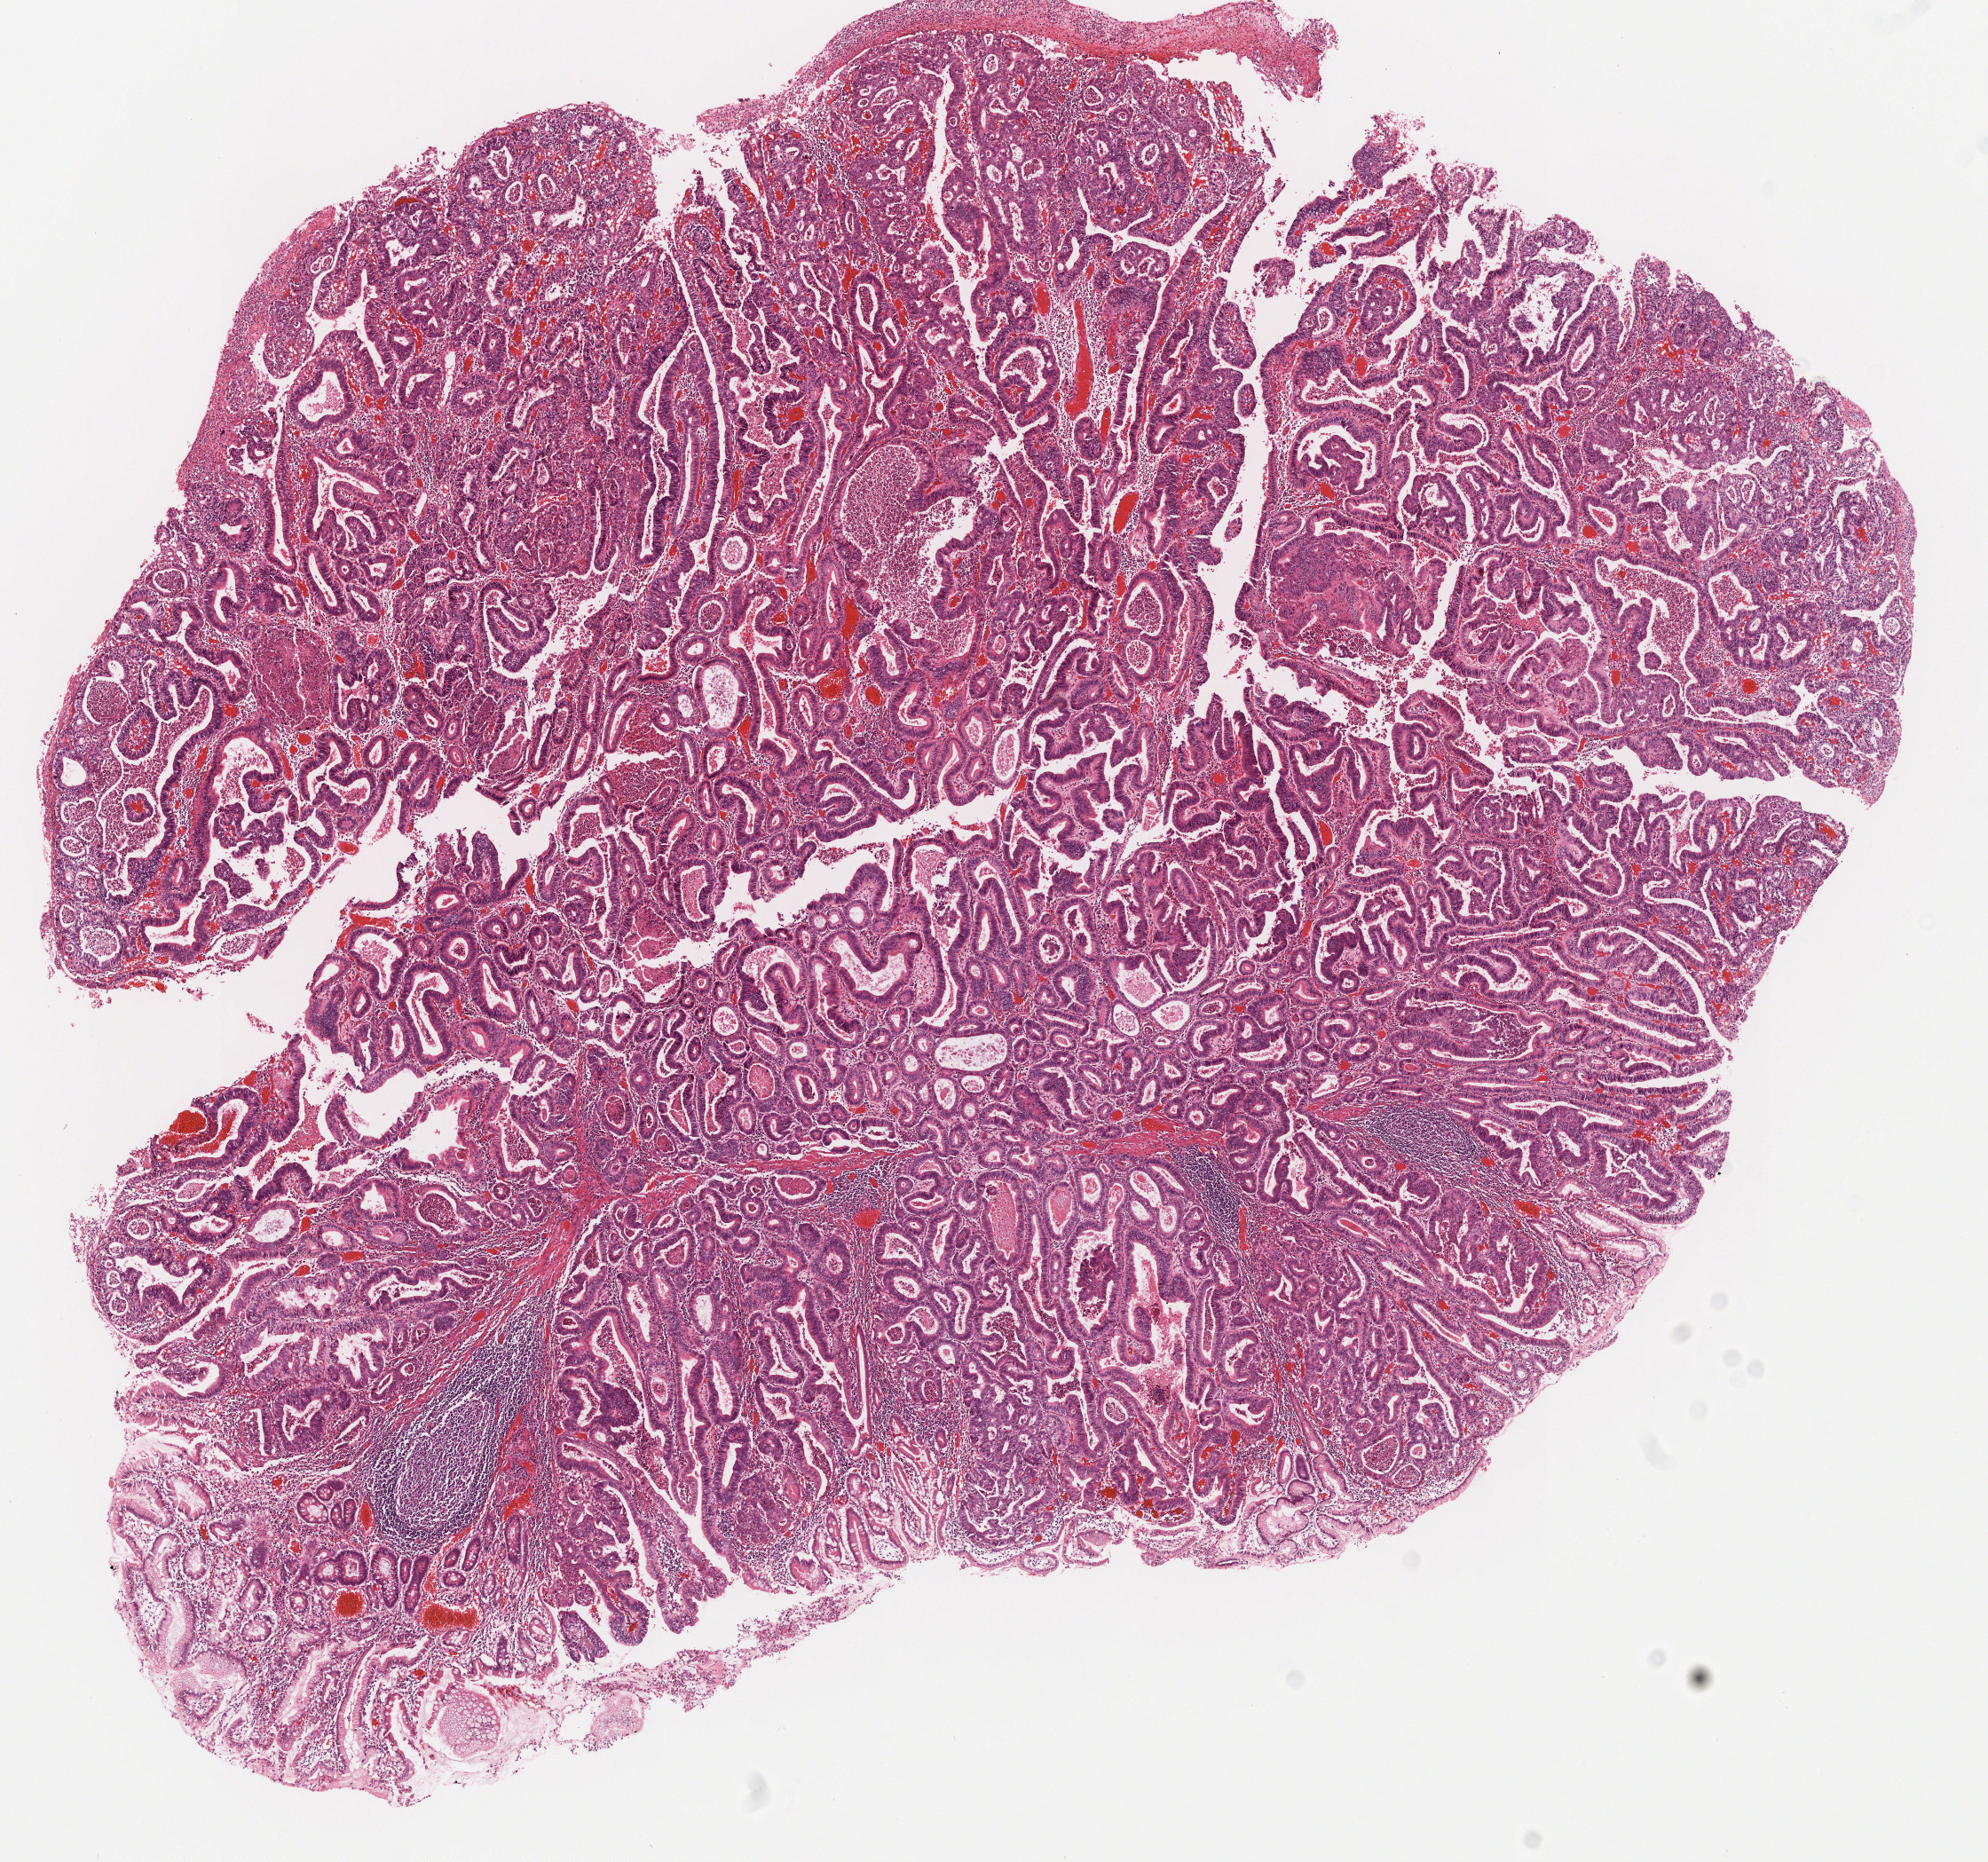
Digitized H&E tissue section (whole slide), a low-resolution overview of the entire scanned area, about 8.9 x 8.3 mm; formalin-fixed paraffin-embedded (FFPE) diagnostic section; stomach, primary tumour sample. Male patient; age at initial diagnosis 69 years.
Pathologic diagnosis: Tubular adenocarcinoma (gastric antrum).